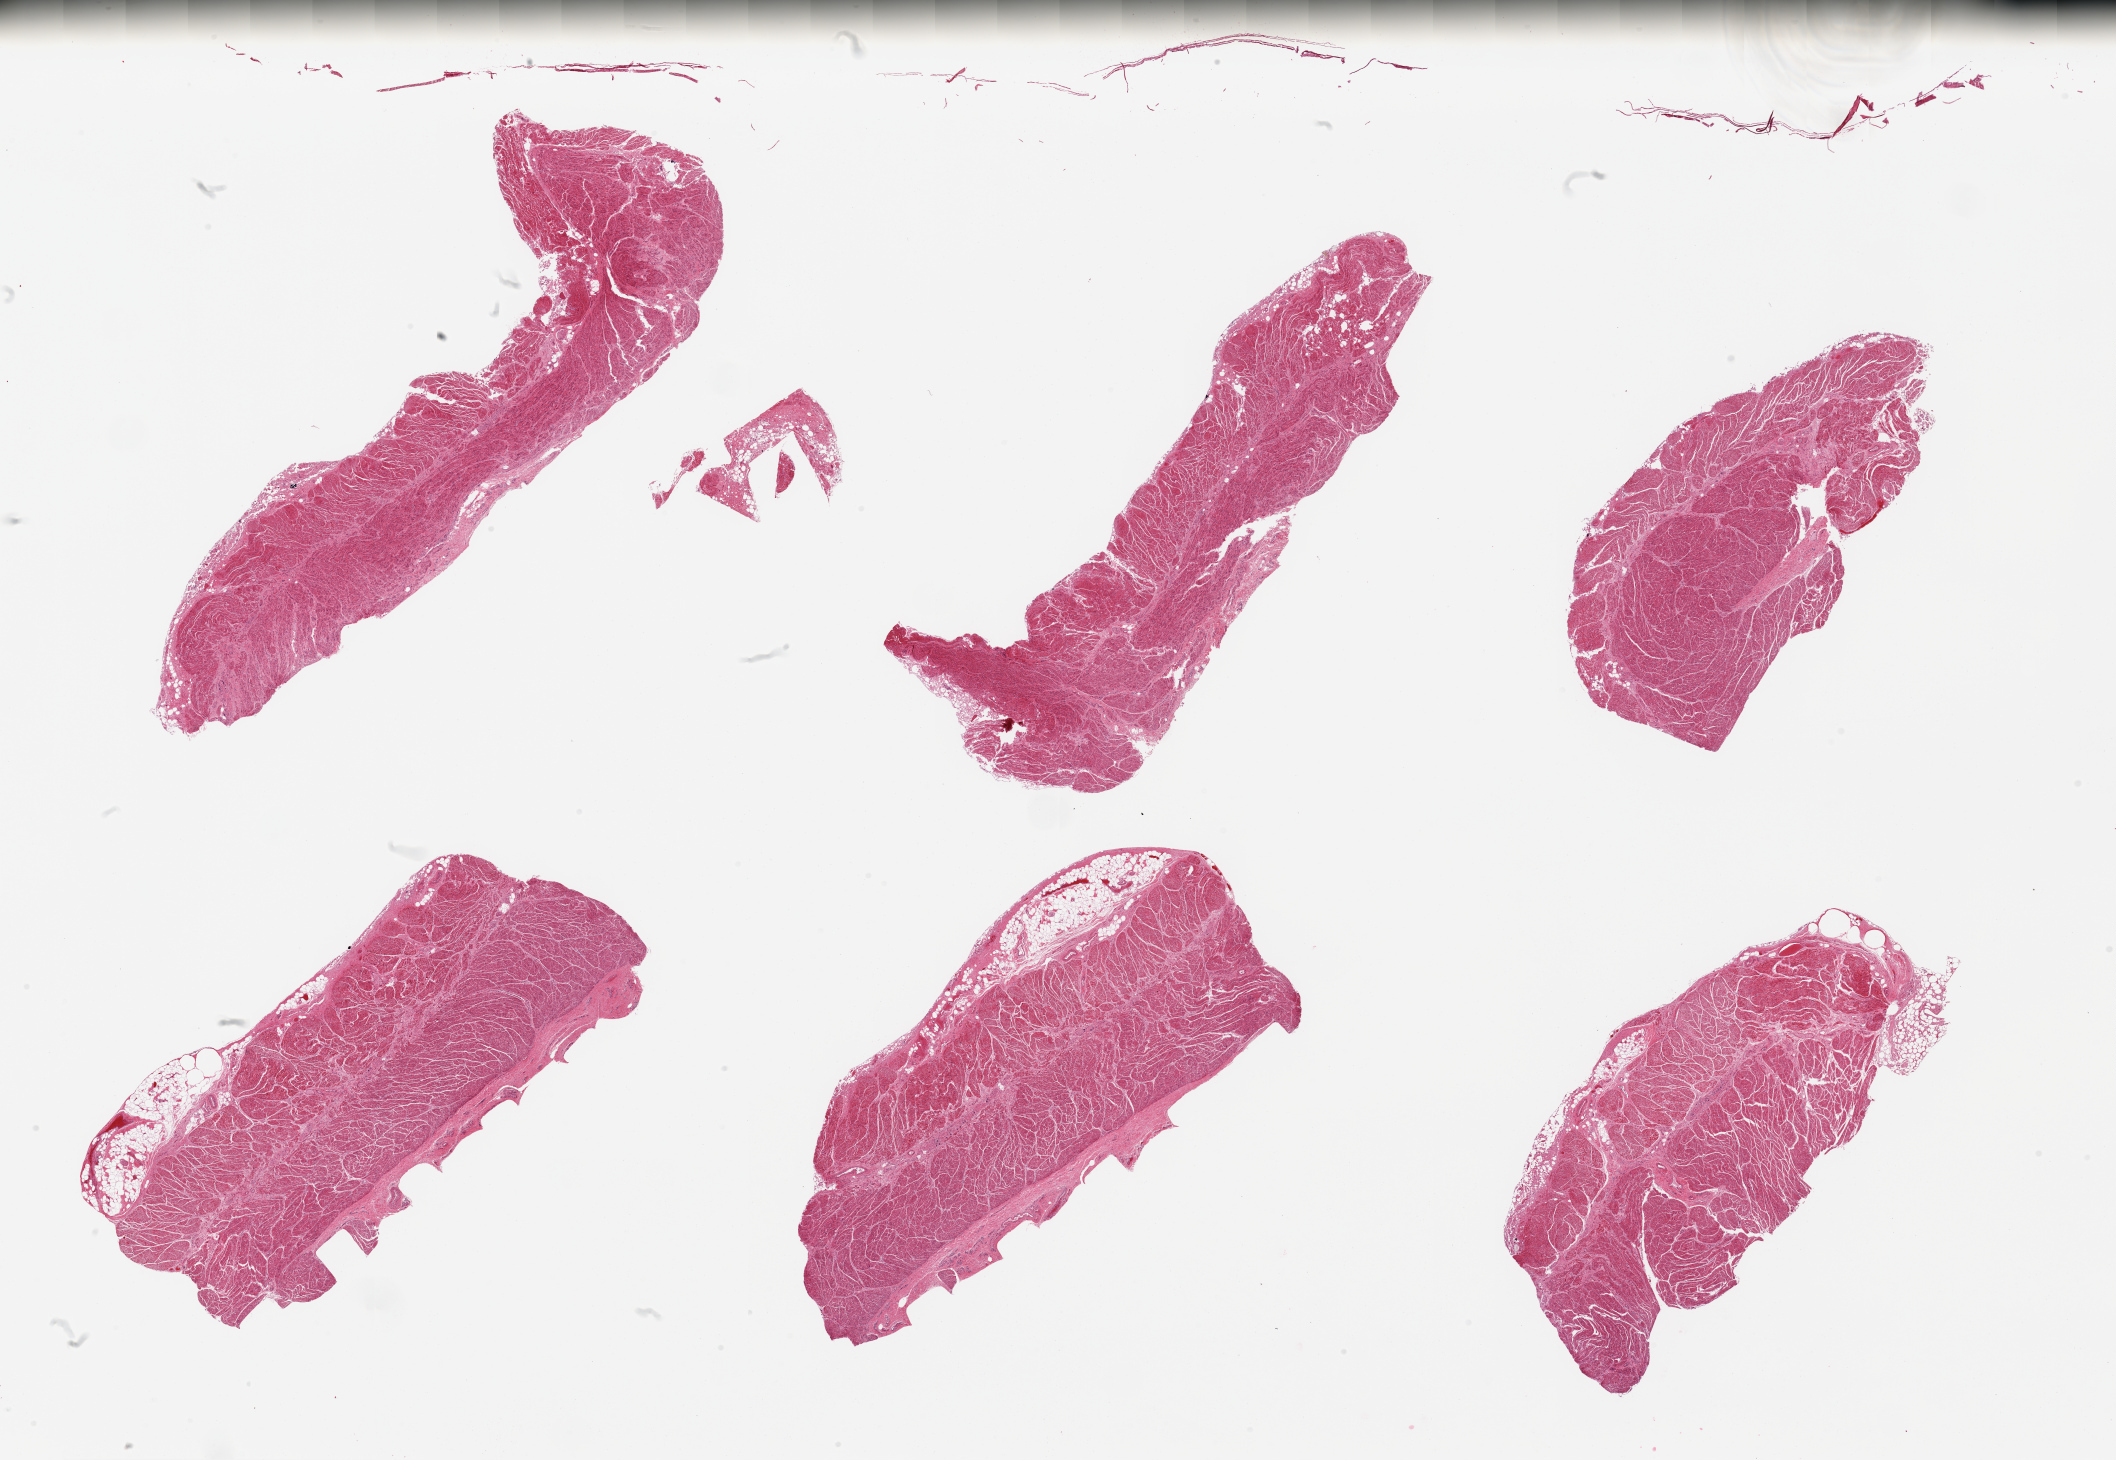
Whole-slide image, haematoxylin and eosin stain — low-resolution overview of the scanned area, about 33.5 x 23.1 mm; PAXgene-fixed, paraffin-embedded tissue; section of gastroesophageal junction (target tissue); donor tissue sample. Donor sex: male.
Reviewer comment on this tissue sample: 6 pieces target muscularis.